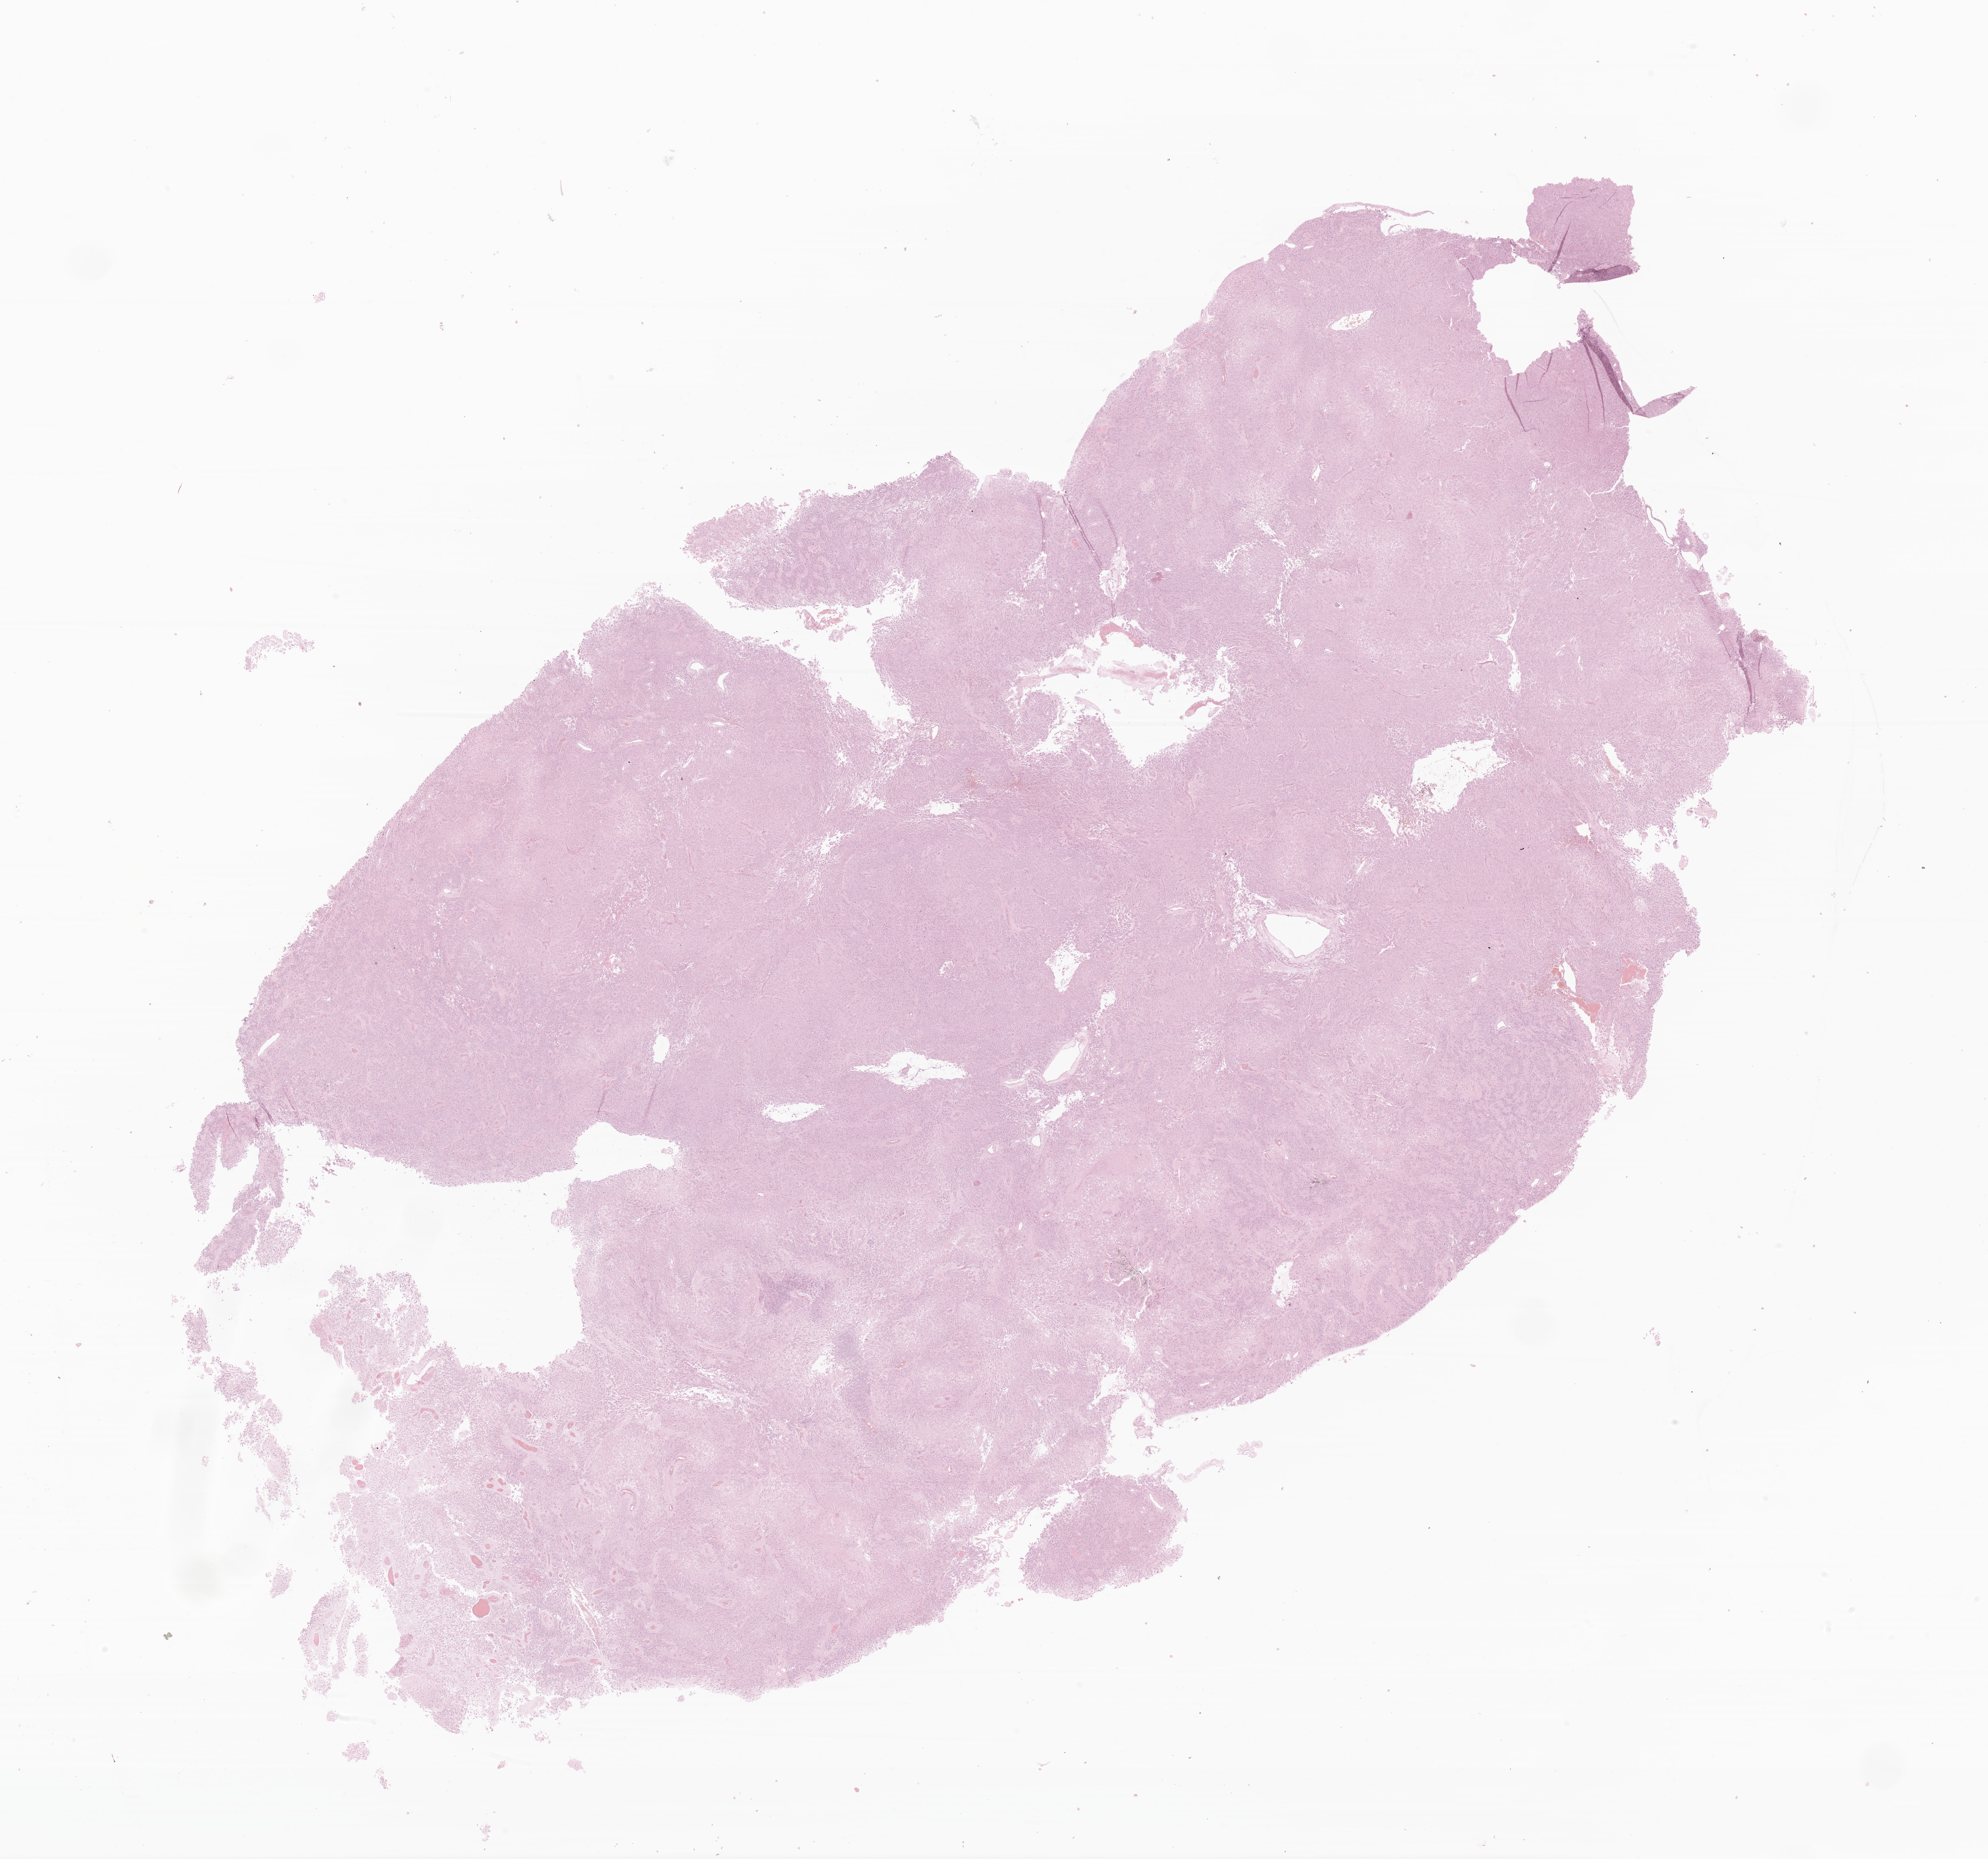
Whole-slide image, haematoxylin and eosin stain of tumor tissue from the brain, a low-resolution overview of the entire scanned area, about 22.8 x 21.4 mm; formalin-fixed paraffin-embedded section. Patient: female, age 119 months (9 years 11 months).
Diagnosis (ICD-O-3 morphology term): Glioma, malignant.